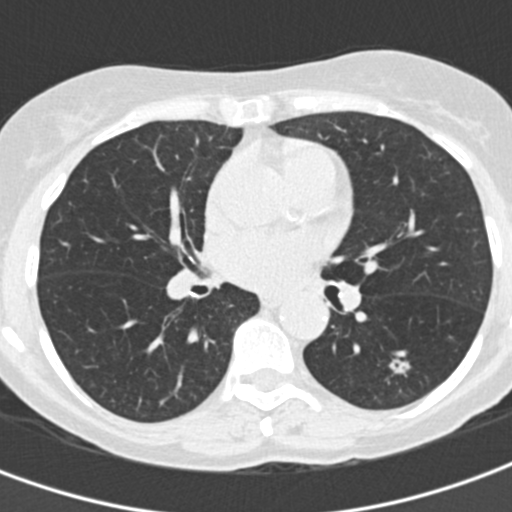
Low-dose screening chest CT, one axial slice; position 81 of 155 along the scan axis; reconstruction kernel B30f; lung window (W 1500 / L -600 HU); 512 × 512 image matrix, field of view 282 × 282 mm.
Outlined on this slice (expert manual segmentation):
- lesion 1 (tumor, lower lobe of left lung): box from (x=389, y=357) to (x=411, y=377) px